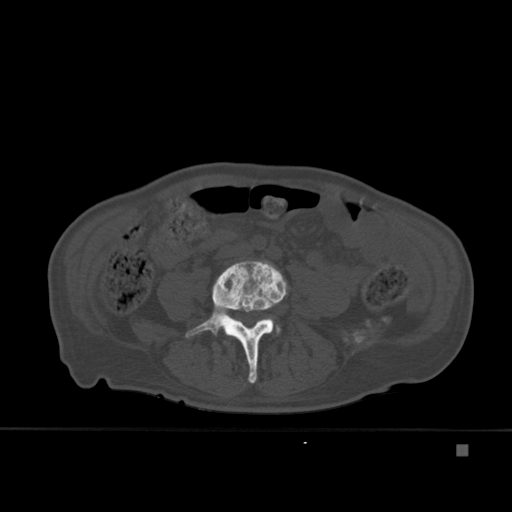
CT including the spine, one axial slice. Slice 121 of 451 in the series (ordered by position). Bone window (W 1800 / L 400 HU). 512 × 512 image matrix, field of view 378 × 378 mm. Patient: male, 75 years. Case-level facts recorded for this patient, not image findings: primary cancer: prostate.
Structures marked on this image (semi-automatically segmented with operator editing):
- L4 vertebra: bounding box <186,260,288,383> (left, top, right, bottom; pixels)
- L5 vertebra: <277,325,281,335>